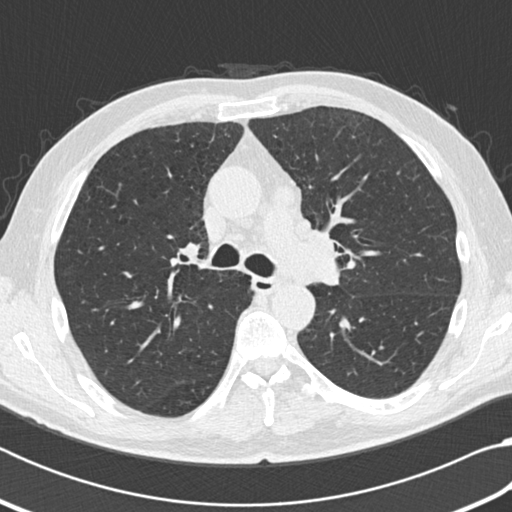
Chest CT (low-dose screening protocol), one axial image; third annual screen; lung window (W 1500 / L -600 HU); 2 mm slice thickness; standard (soft-tissue) reconstruction kernel (B30f); slice 74 of 207 in the series. Male participant, aged 64 years at enrolment. Current smoker at enrolment.
Expert-annotated lung lesion, bounding box <253,175,304,221> (left, top, right, bottom; pixels). Screening reader's record for this exam: no non-calcified nodule ≥4 mm recorded.